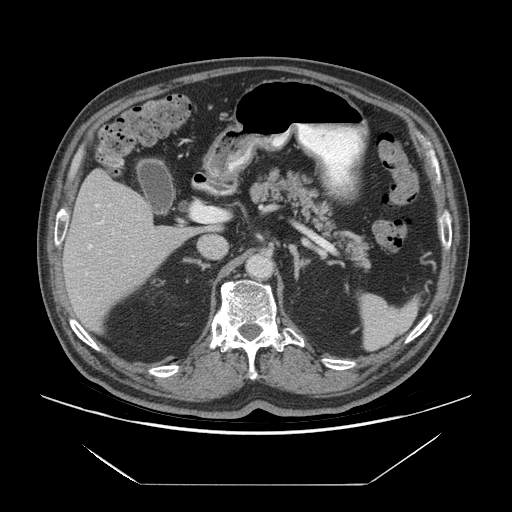
Contrast-enhanced abdominal CT (liver protocol), one axial slice. Slice 35 of 75 in the series (ordered by position). 140 kVp. Soft-tissue window (W 400 / L 40 HU). 2.5 mm slice thickness. 512 × 512 image matrix. Case-level facts recorded for this patient, not image findings: diagnosis: hepatocellular carcinoma (patient treated with transarterial chemoembolisation; whether this scan precedes or follows treatment is not stated here); TNM stage (as recorded): Stage-I; Child-Pugh class: A.
Structures marked on this image (semi-automatic segmentation, software-assisted and operator-edited):
- liver parenchyma outside the tumour (the mass and vessels are separate outlines, so this box may not span the whole liver): bounding box (x1, y1, x2, y2) in pixels: (62, 169, 194, 332)
- liver vessels: (86, 204, 121, 275)